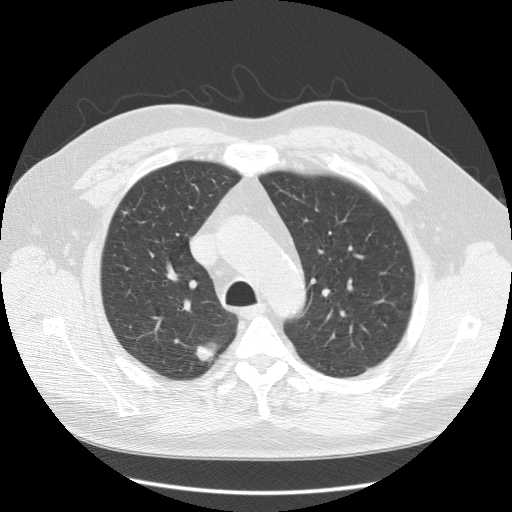
Low-dose screening chest CT, axial slice, first (baseline) screen, lung window (W 1500 / L -600 HU), 2.5 mm slice thickness, standard (soft-tissue) reconstruction kernel (STANDARD), 512 × 512 image matrix, field of view 380 × 380 mm. Male participant, aged 55 years at enrolment. Former smoker at enrolment.
• Expert-annotated lung lesion, bounding box [x1, y1, x2, y2] px = [184, 331, 231, 376].
• The screening reader recorded 2 non-calcified nodules or masses ≥4 mm on this exam; which of them this box marks is not recorded.
• Participant outcome: lung cancer diagnosed 84 days after this screen — large cell neuroendocrine carcinoma, right upper lobe, poorly differentiated (G3), stage IA (AJCC 6th edition), 18 mm at pathology.